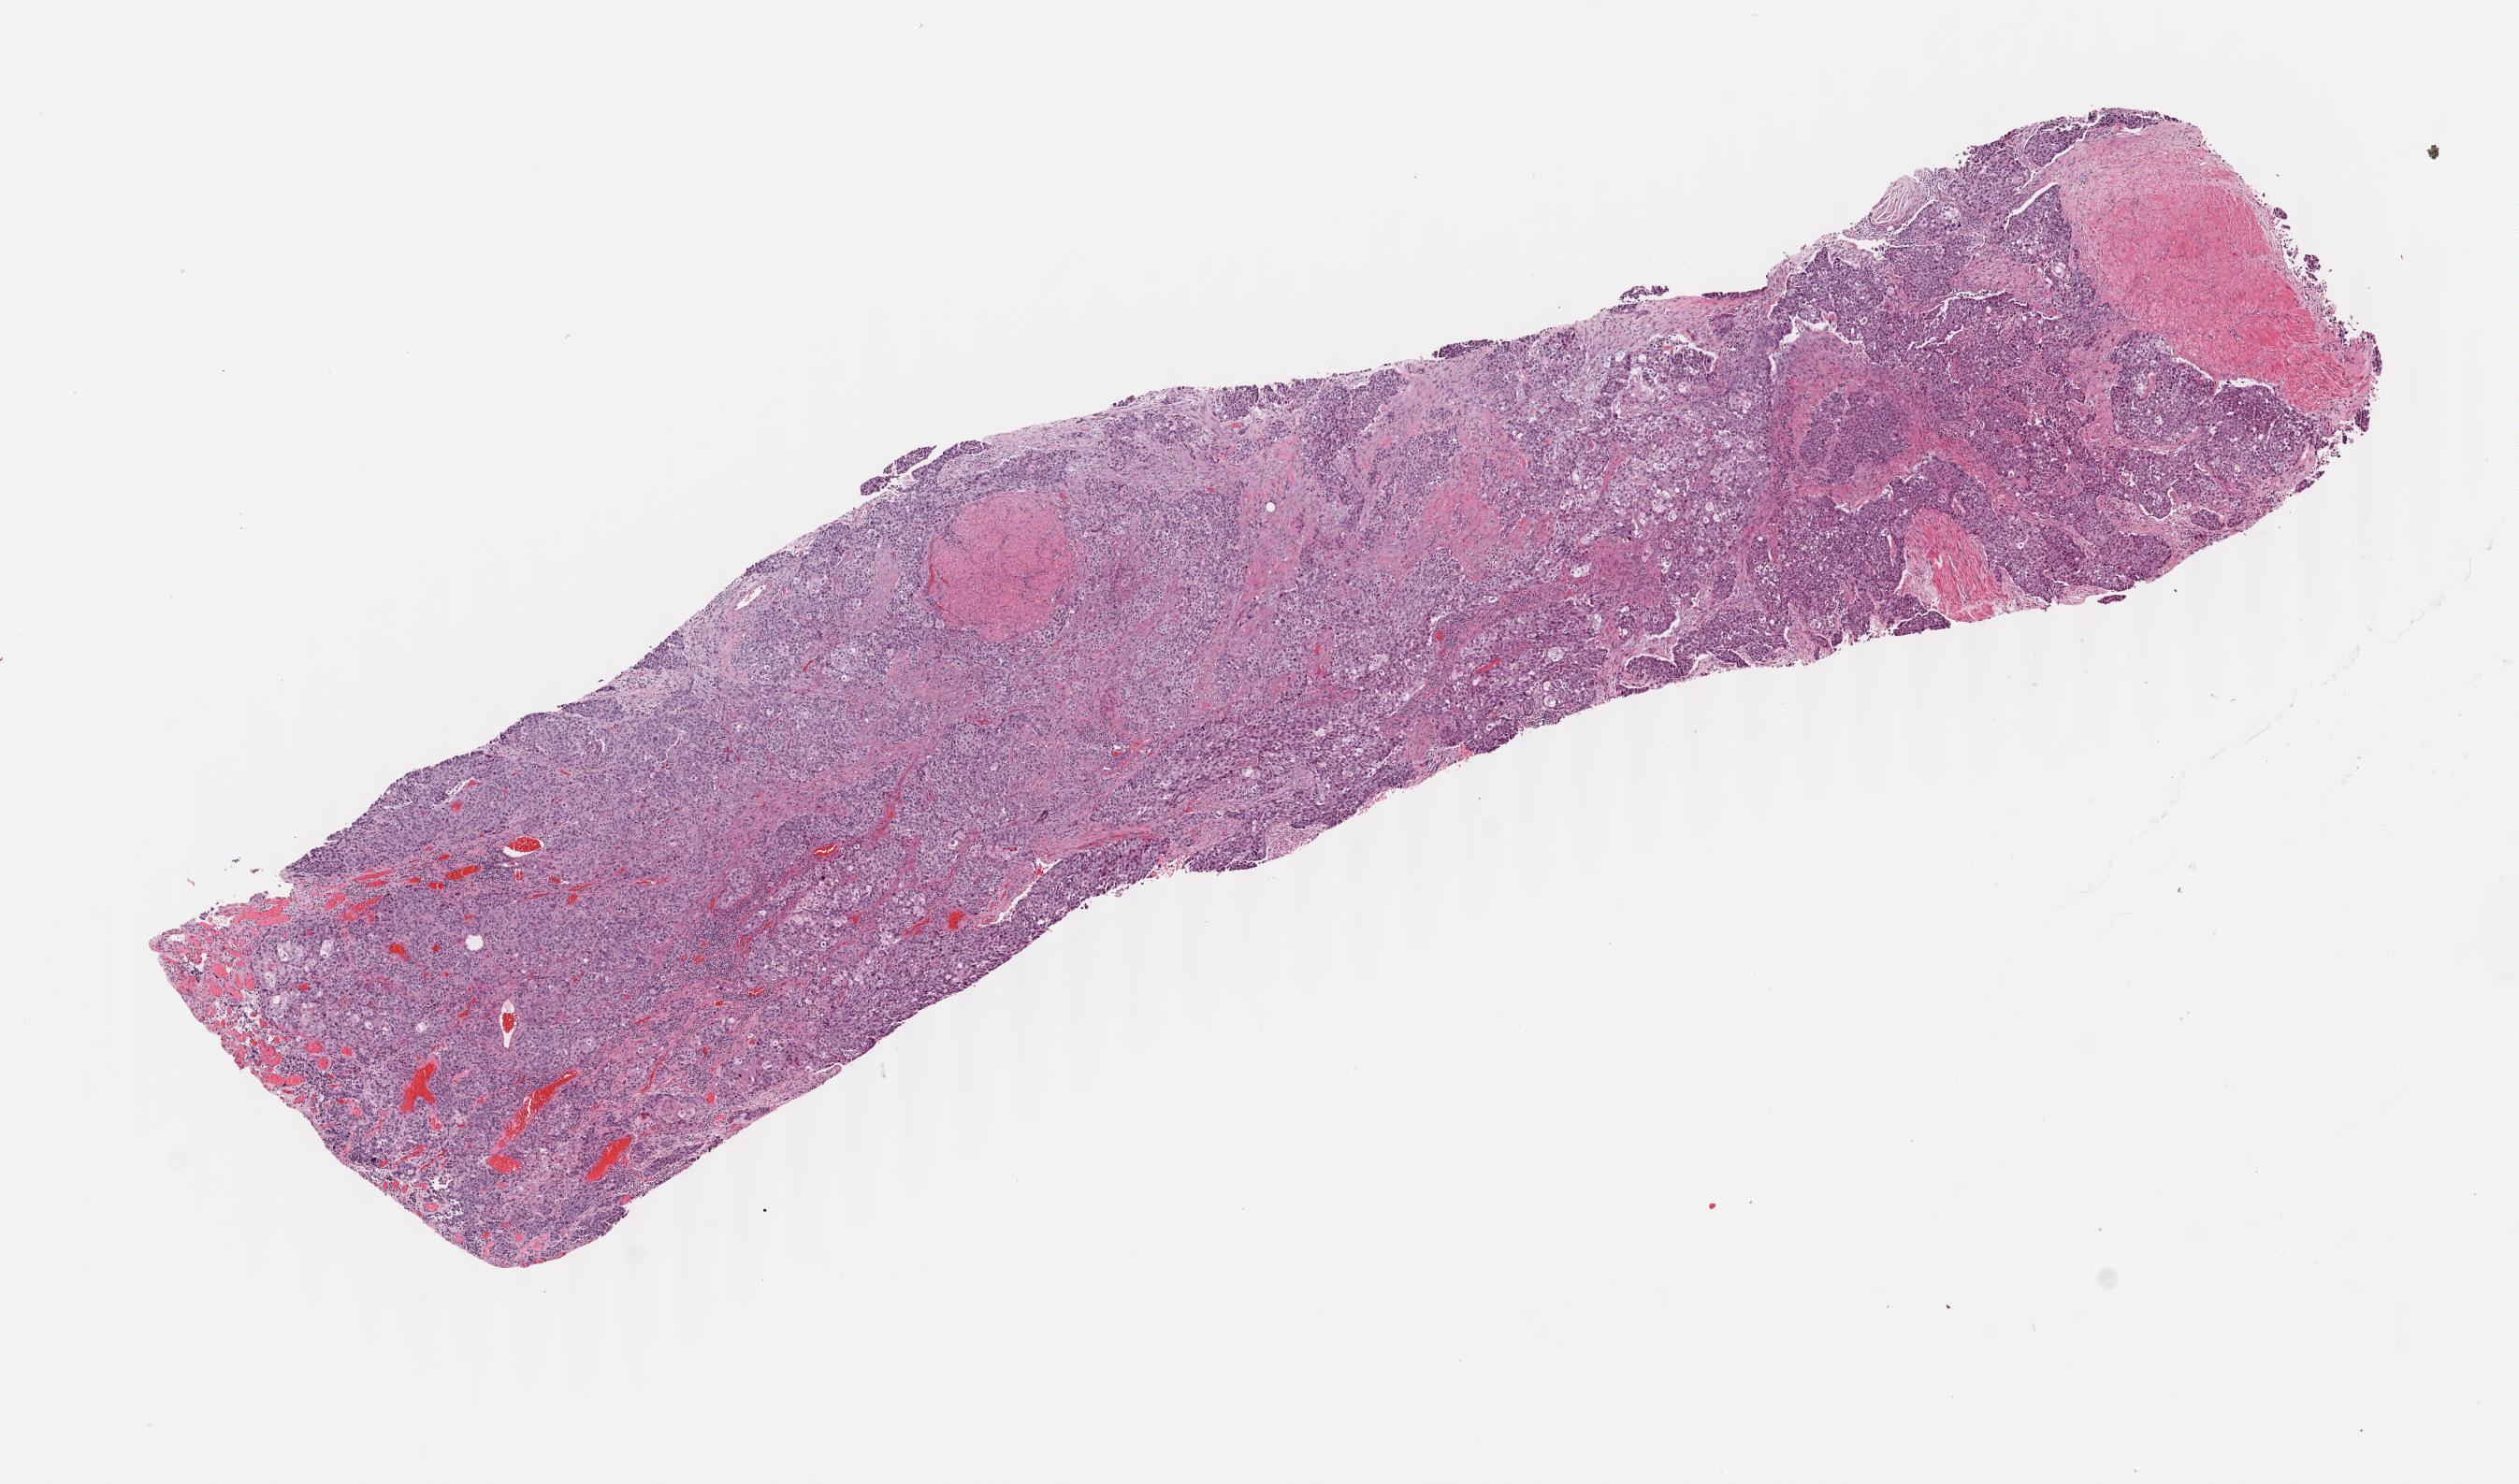
Whole-slide histology image, H&E — whole scanned area (about 10.7 x 6.3 mm, from a 40x scan) shown as a low-resolution overview. Frozen section. Sample: primary tumour, bladder. Patient: male, age at initial diagnosis 65 years. Histologic grade: high grade. Pathologist review of this section (percent, as recorded): tumour cells 80%, tumour nuclei 80%, normal cells 15%, stromal cells 5%, necrosis 0%. Infiltration values recorded for this section: lymphocyte infiltration 0%, monocyte infiltration 0%, neutrophil infiltration 0%.
Histologic diagnosis: Transitional cell carcinoma (posterior wall of bladder). Lymph nodes positive (case pathology): 2 of 11 examined. TNM: T4 N2 M0. AJCC pathologic stage: IV.